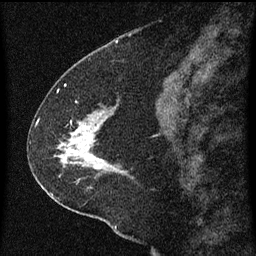
Breast MRI (dynamic contrast-enhanced), one sagittal slice; position 29 of 60 along the scan axis; dynamic contrast-enhanced series, image 2 of 3 at this slice position (ordered by acquisition); 1.5 T; TE 4.2 ms, TR 8 ms; 256 × 256 image matrix, field of view 180 × 180 mm. Patient: female, 47 years.
Annotated regions visible in this slice (semi-automatically segmented with operator editing):
- analysis volume of interest (the breast-tissue region the enhancement analysis was run in; not a lesion): box from (x=36, y=96) to (x=136, y=213) px
- tumour enhancement mask (voxels above the 70 % enhancement threshold inside the analysis volume of interest): (x=58, y=116)–(x=107, y=169)